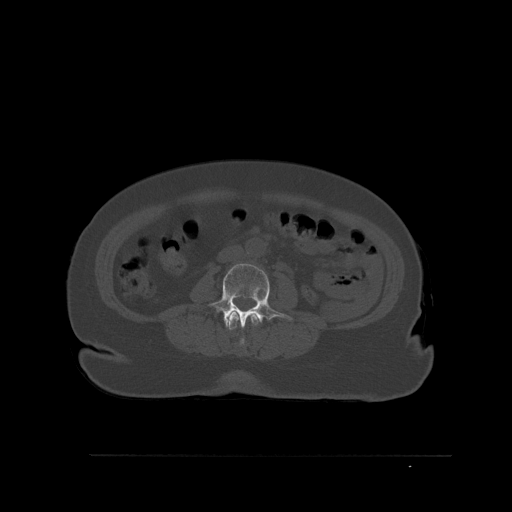
CT including the spine, one axial slice; position 227 of 527 along the scan axis; bone window (W 1800 / L 400 HU); 512 × 512 image matrix, field of view 470 × 470 mm. Female patient, age 73 years. Case-level facts recorded for this patient, not image findings: primary cancer: breast; vertebrae with lytic lesions (as recorded): L2.
Outlined on this slice (semi-automatically segmented with operator editing):
- L2 vertebra: bounding box <227,312,259,347> (left, top, right, bottom; pixels)
- L3 vertebra: <207,263,293,328>